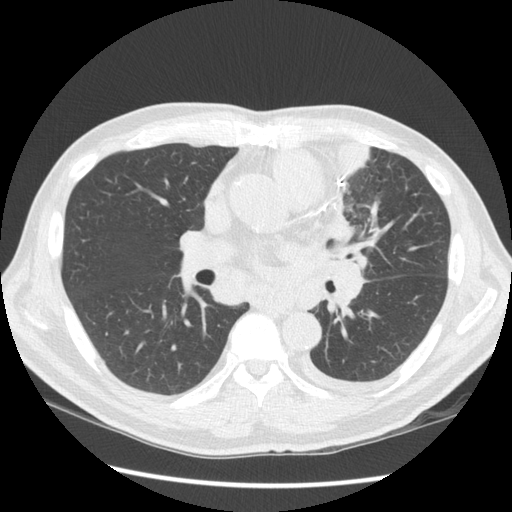
Low-dose screening chest CT, one axial slice. Slice 77 of 136 in the series (ordered by position). Reconstruction kernel STANDARD. 120 kVp. Lung window (W 1500 / L -600 HU). 2.5 mm slice thickness. 512 × 512 image matrix, field of view 360 × 360 mm.
Annotated regions visible in this slice (expert manual segmentation):
- lesion 1 (tumor, upper lobe of left lung): bounding box <320,140,369,252> (left, top, right, bottom; pixels)